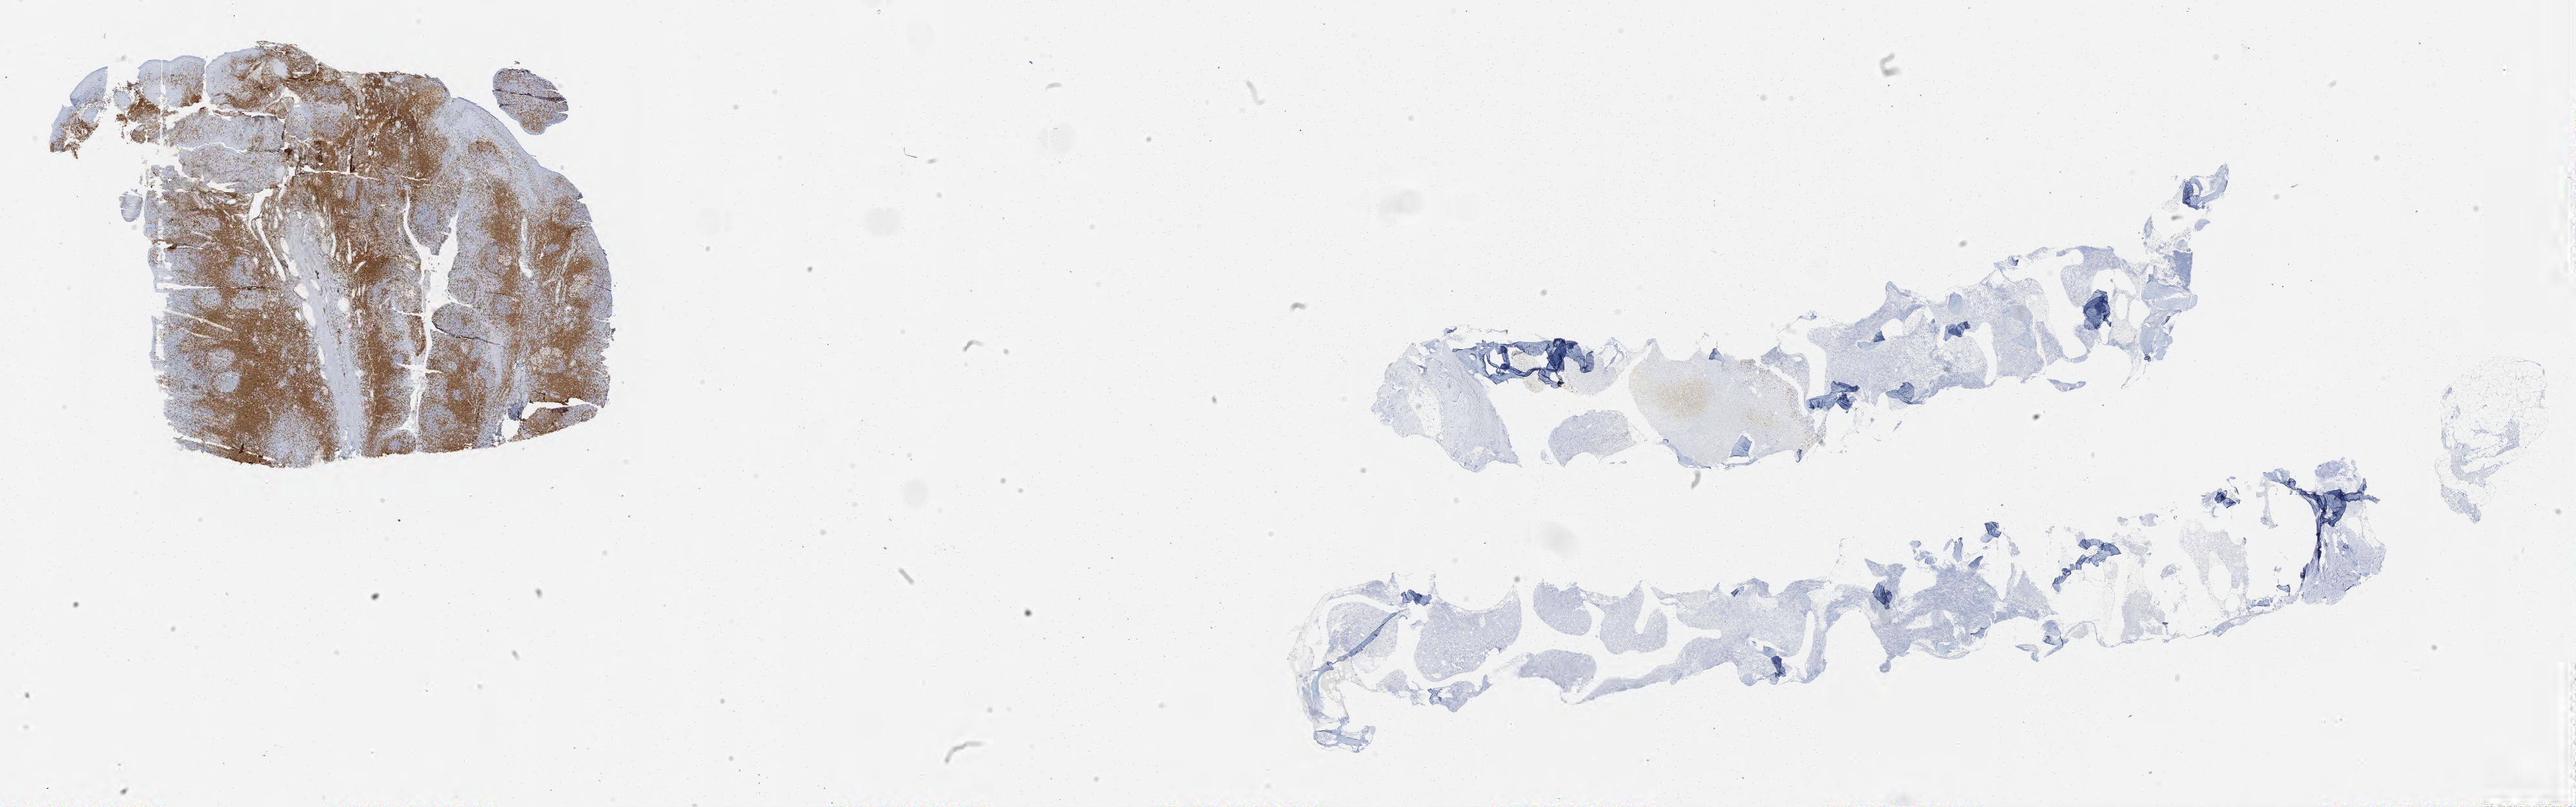
Whole-slide image, immunohistochemical stain for CD3, whole scanned area (about 32.0 x 10.0 mm) shown as a low-resolution overview; tumor tissue. Female patient, 60 years old.
• histologic diagnosis: Burkitt lymphoma, NOS